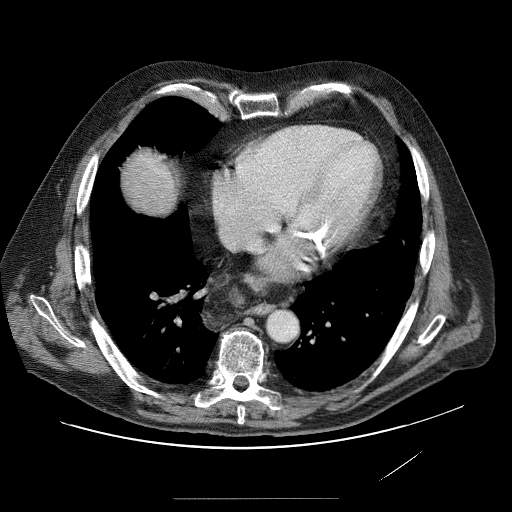
Contrast-enhanced abdominal CT (liver protocol), one axial slice; reconstruction kernel STANDARD; 120 kVp; soft-tissue window (W 400 / L 40 HU); 2.5 mm slice thickness; 512 × 512 image matrix, field of view 420 × 420 mm. From the clinical record (not read from this slice): diagnosis: hepatocellular carcinoma (patient treated with transarterial chemoembolisation; whether this scan precedes or follows treatment is not stated here); TNM stage (as recorded): Stage-IVA; Child-Pugh class: A; tumour differentiation: moderately differentiated.
Outlined on this slice (semi-automatic segmentation, software-assisted and operator-edited):
- liver parenchyma outside the tumour (the mass and vessels are separate outlines, so this box may not span the whole liver): bounding box <138,164,168,194> (left, top, right, bottom; pixels)